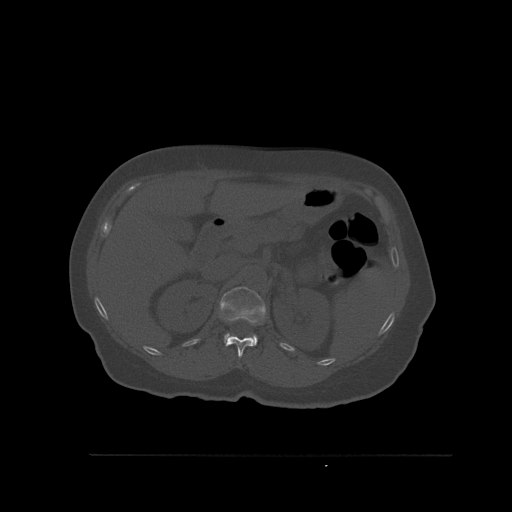
CT including the spine, one axial slice. Slice 278 of 527 in the series (ordered by position). Bone window (W 1800 / L 400 HU). 1.5 mm slice thickness. 512 × 512 image matrix, field of view 470 × 470 mm. Female patient, age 73 years. From the clinical record (not read from this slice): primary cancer: breast.
Annotated regions visible in this slice (semi-automatic segmentation, software-assisted and operator-edited):
- L1 vertebra: box from (x=219, y=286) to (x=266, y=346) px
- T12 vertebra: (x=226, y=336)–(x=253, y=358)